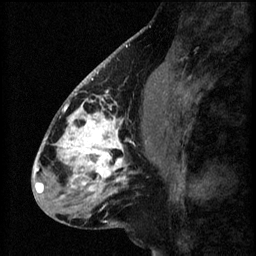
Breast MRI (dynamic contrast-enhanced), one sagittal slice; position 27 of 60 along the scan axis; 3 images stored at this slice position (order not interpretable as contrast timing); 1.5 T; TE 4.2 ms, TR 8.2 ms; 2.2 mm slice thickness; 256 × 256 image matrix, field of view 180 × 180 mm. Patient: female, 41 years.
Annotated regions visible in this slice (semi-automatic segmentation, software-assisted and operator-edited):
- analysis volume of interest (the breast-tissue region the enhancement analysis was run in; not a lesion): bounding box (x1, y1, x2, y2) in pixels: (56, 104, 157, 207)
- tumour enhancement mask (voxels above the 70 % enhancement threshold inside the analysis volume of interest): (56, 104, 134, 199)